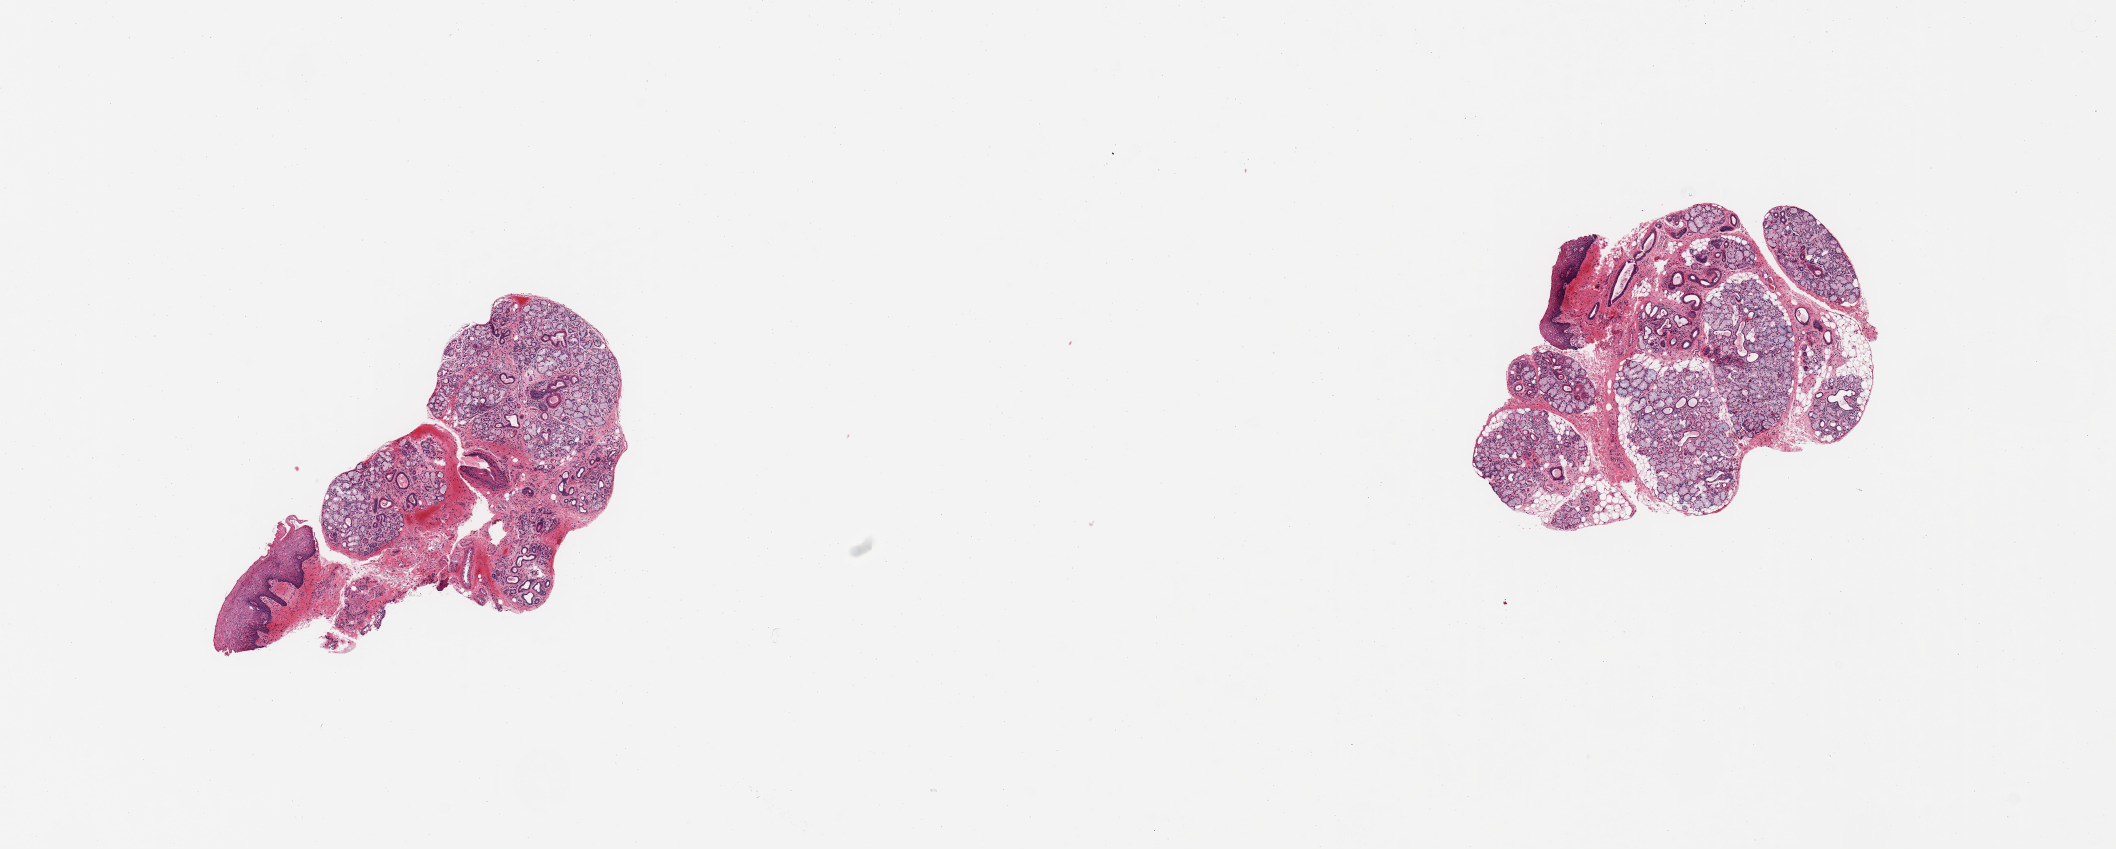
H&E whole-slide image, brightfield, low-resolution overview of the scanned area, about 16.7 x 6.7 mm (slide scanned at 20x), PAXgene-fixed, paraffin-embedded tissue, sampled site (target tissue): minor salivary gland, donor tissue sample.
Pathologist's review note for this sample: 2 pieces; lobules of salivary gland with attached squamous epithelium/lip, small amount of fat admixed, mild chronic inflammation.